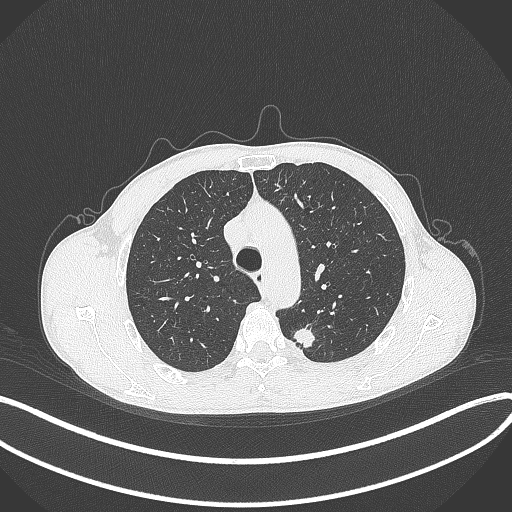
Chest CT, one axial slice; position 294 of 429 along the scan axis; reconstruction kernel B70f; 120 kVp; lung window (W 1500 / L -600 HU); 1 mm slice thickness; 512 × 512 image matrix, field of view 400 × 400 mm. Male patient, age 51 years. Case-level facts recorded for this patient, not image findings: clinical TNM (as recorded): T2a N1 M1.
Annotated regions visible in this slice (rectangle marked by the reading radiologist):
- lung tumour (recorded histology: adenocarcinoma): bounding box <293,325,318,351> (left, top, right, bottom; pixels)